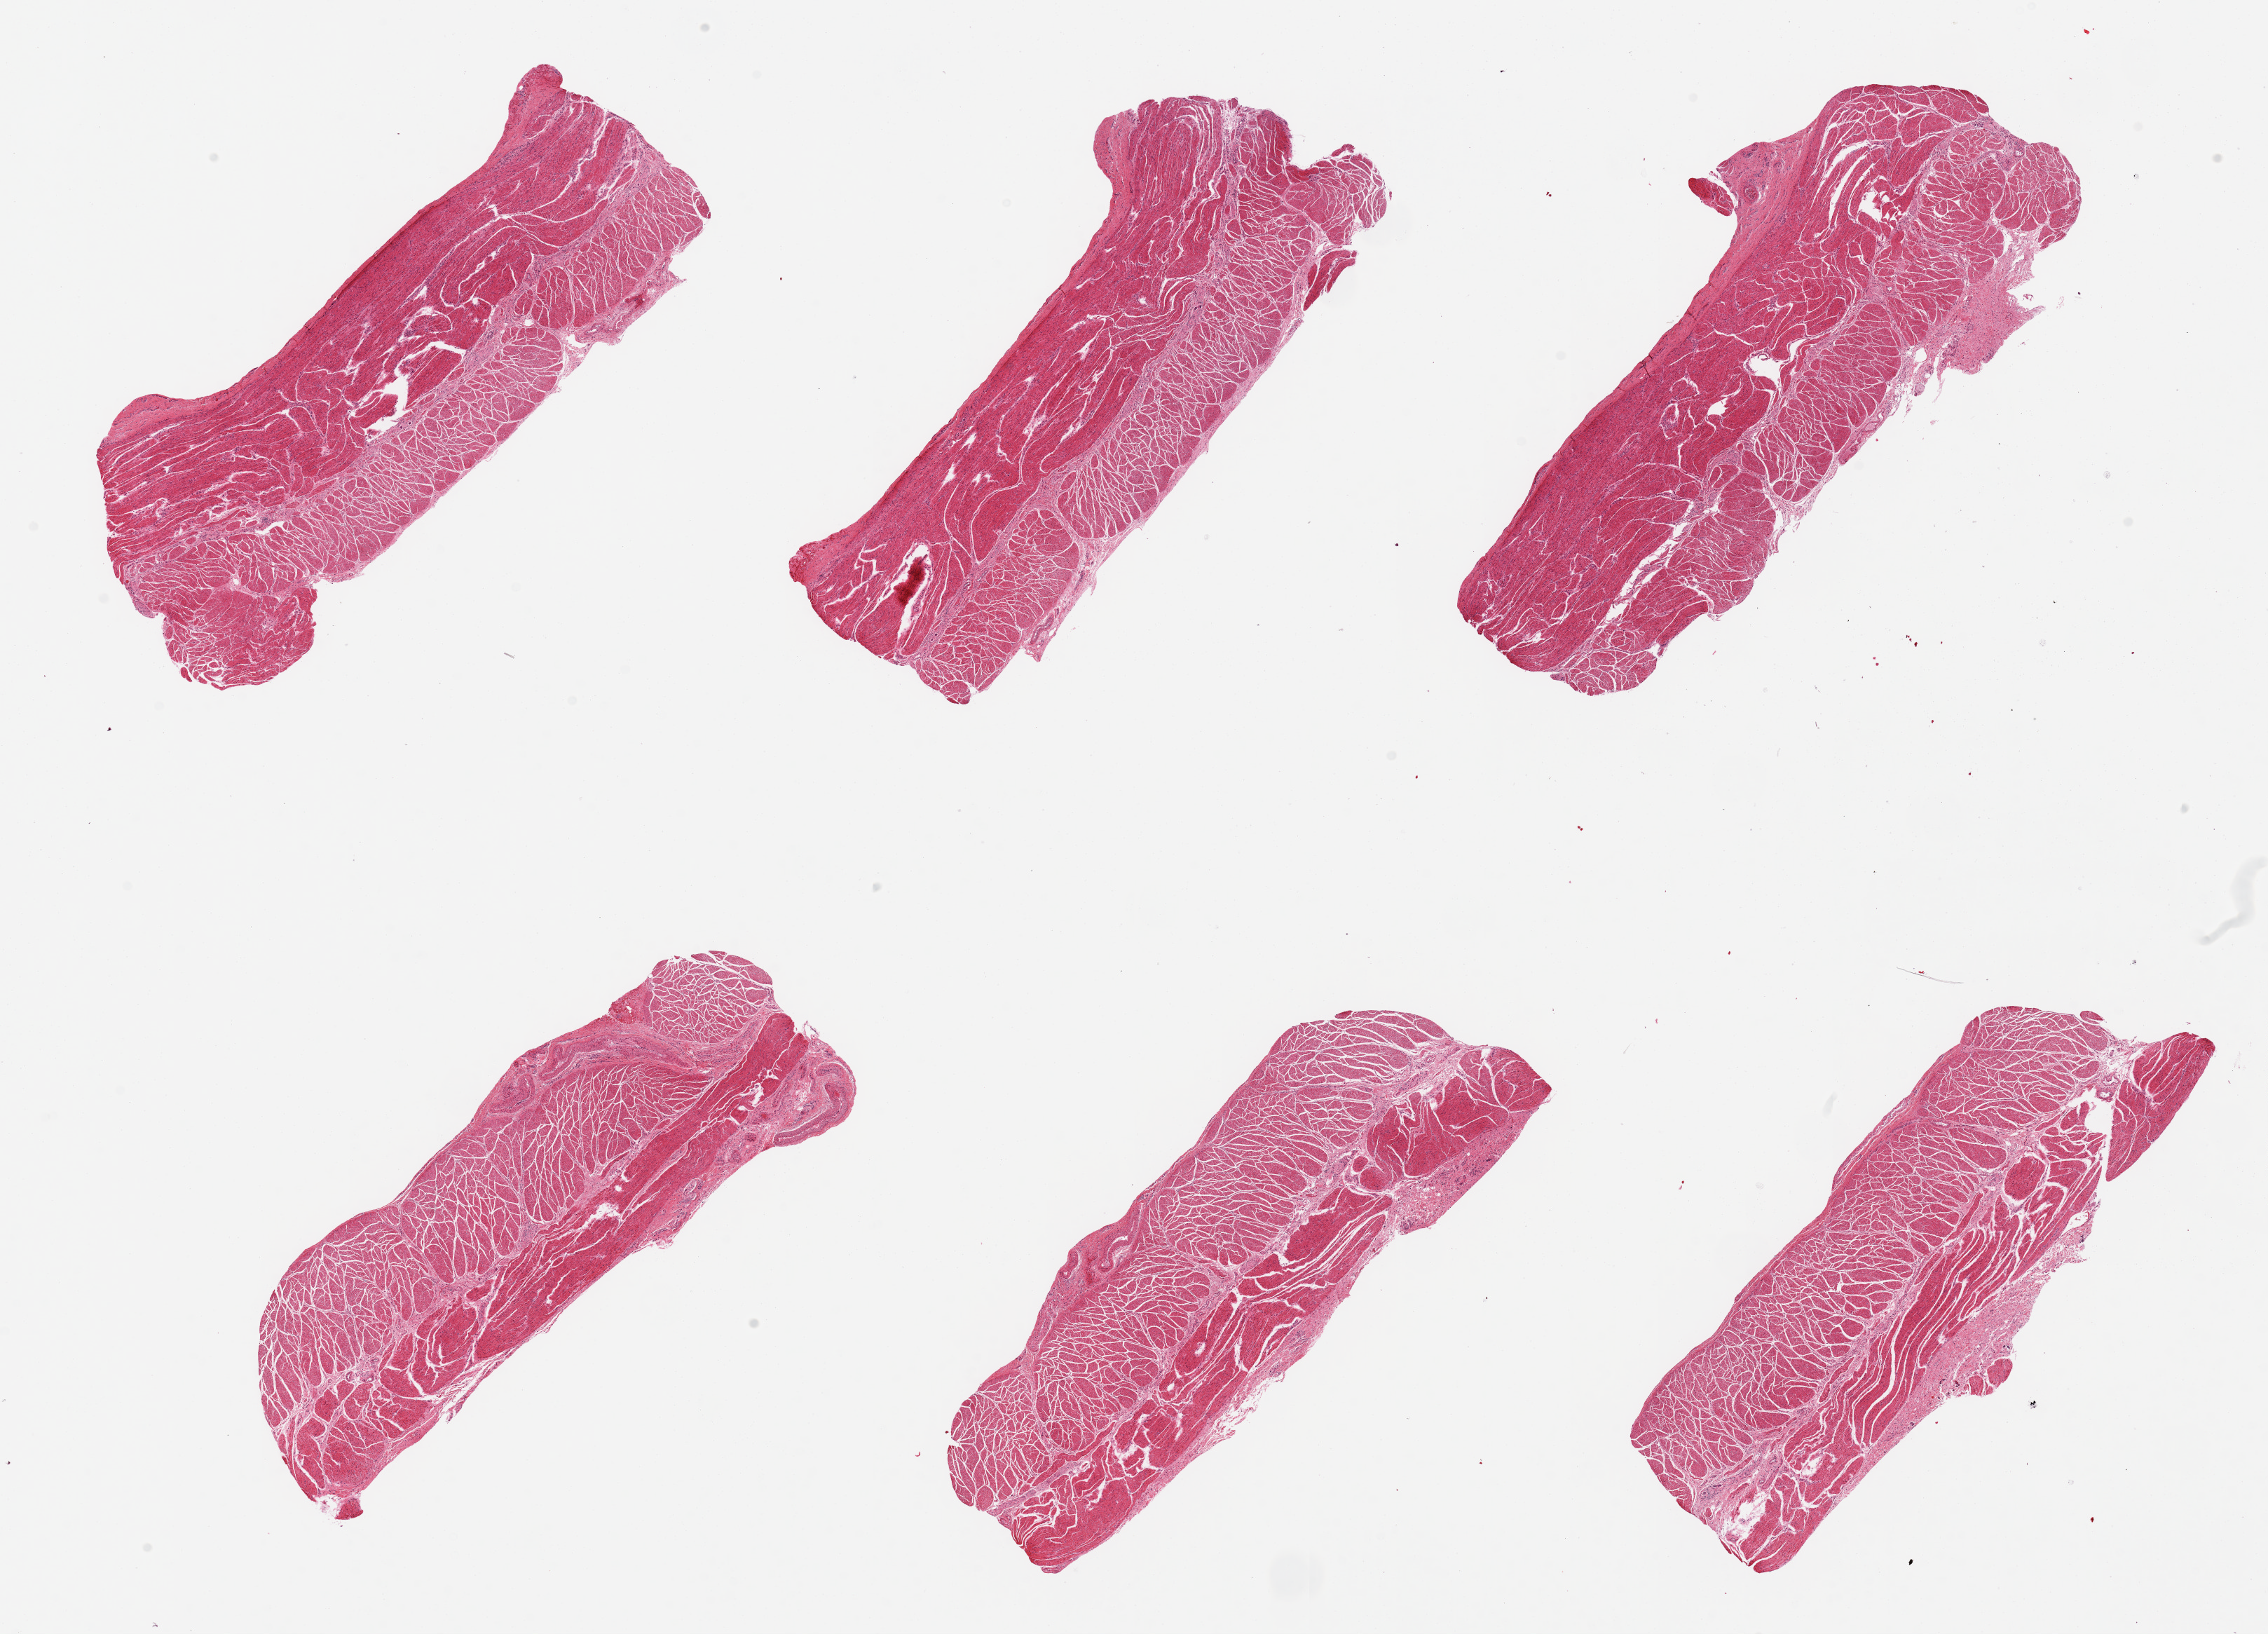
Digitized hematoxylin and eosin (H&E)-stained section, a low-resolution overview of the entire scanned area, about 25.6 x 18.4 mm (acquisition: 20x scan), PAXgene-fixed, paraffin-embedded tissue, section of esophageal muscle (target tissue), donor tissue sample. Donor: female.
Reviewer comment on this tissue sample: 6 pieces, all muscularis, good specimens.